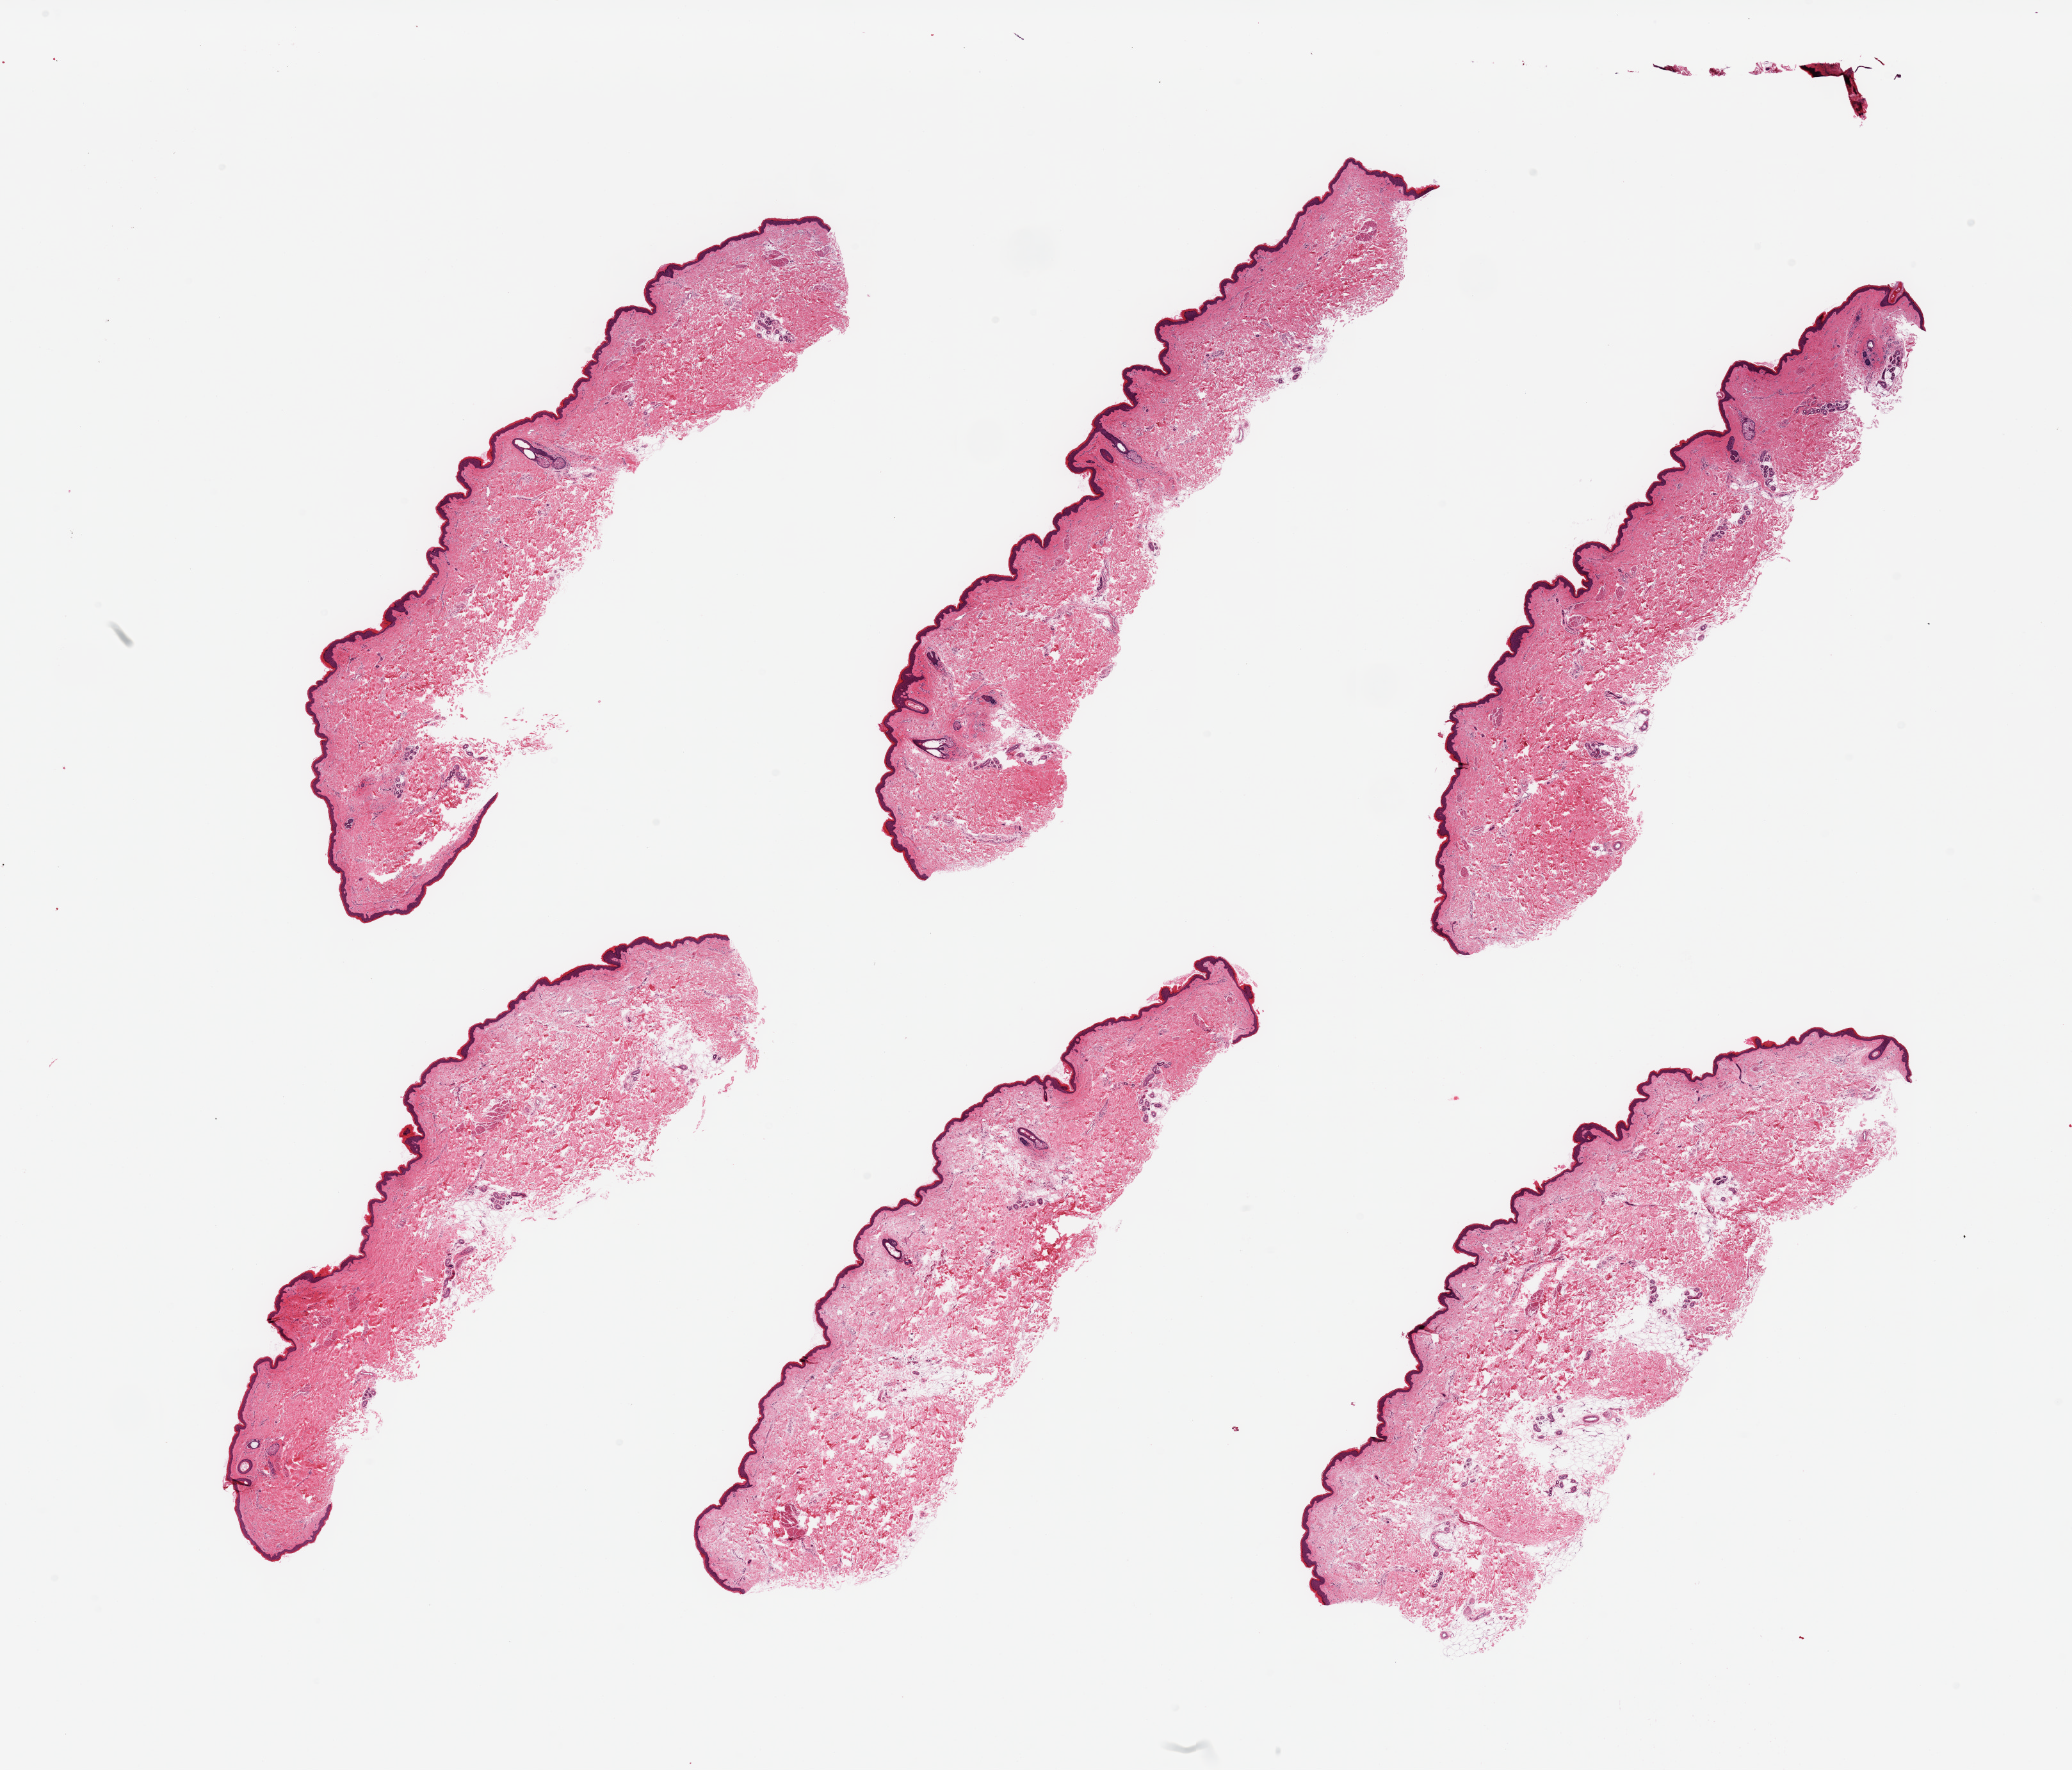
Whole-slide image, haematoxylin and eosin stain, whole scanned area (about 25.6 x 21.9 mm) shown as a low-resolution overview; PAXgene-fixed, paraffin-embedded tissue; target tissue: skin of lower leg; tissue donor sample. Donor sex: male.
• pathologist's review note for this sample: 6 pieces; well trimmed; 10% dermal fat